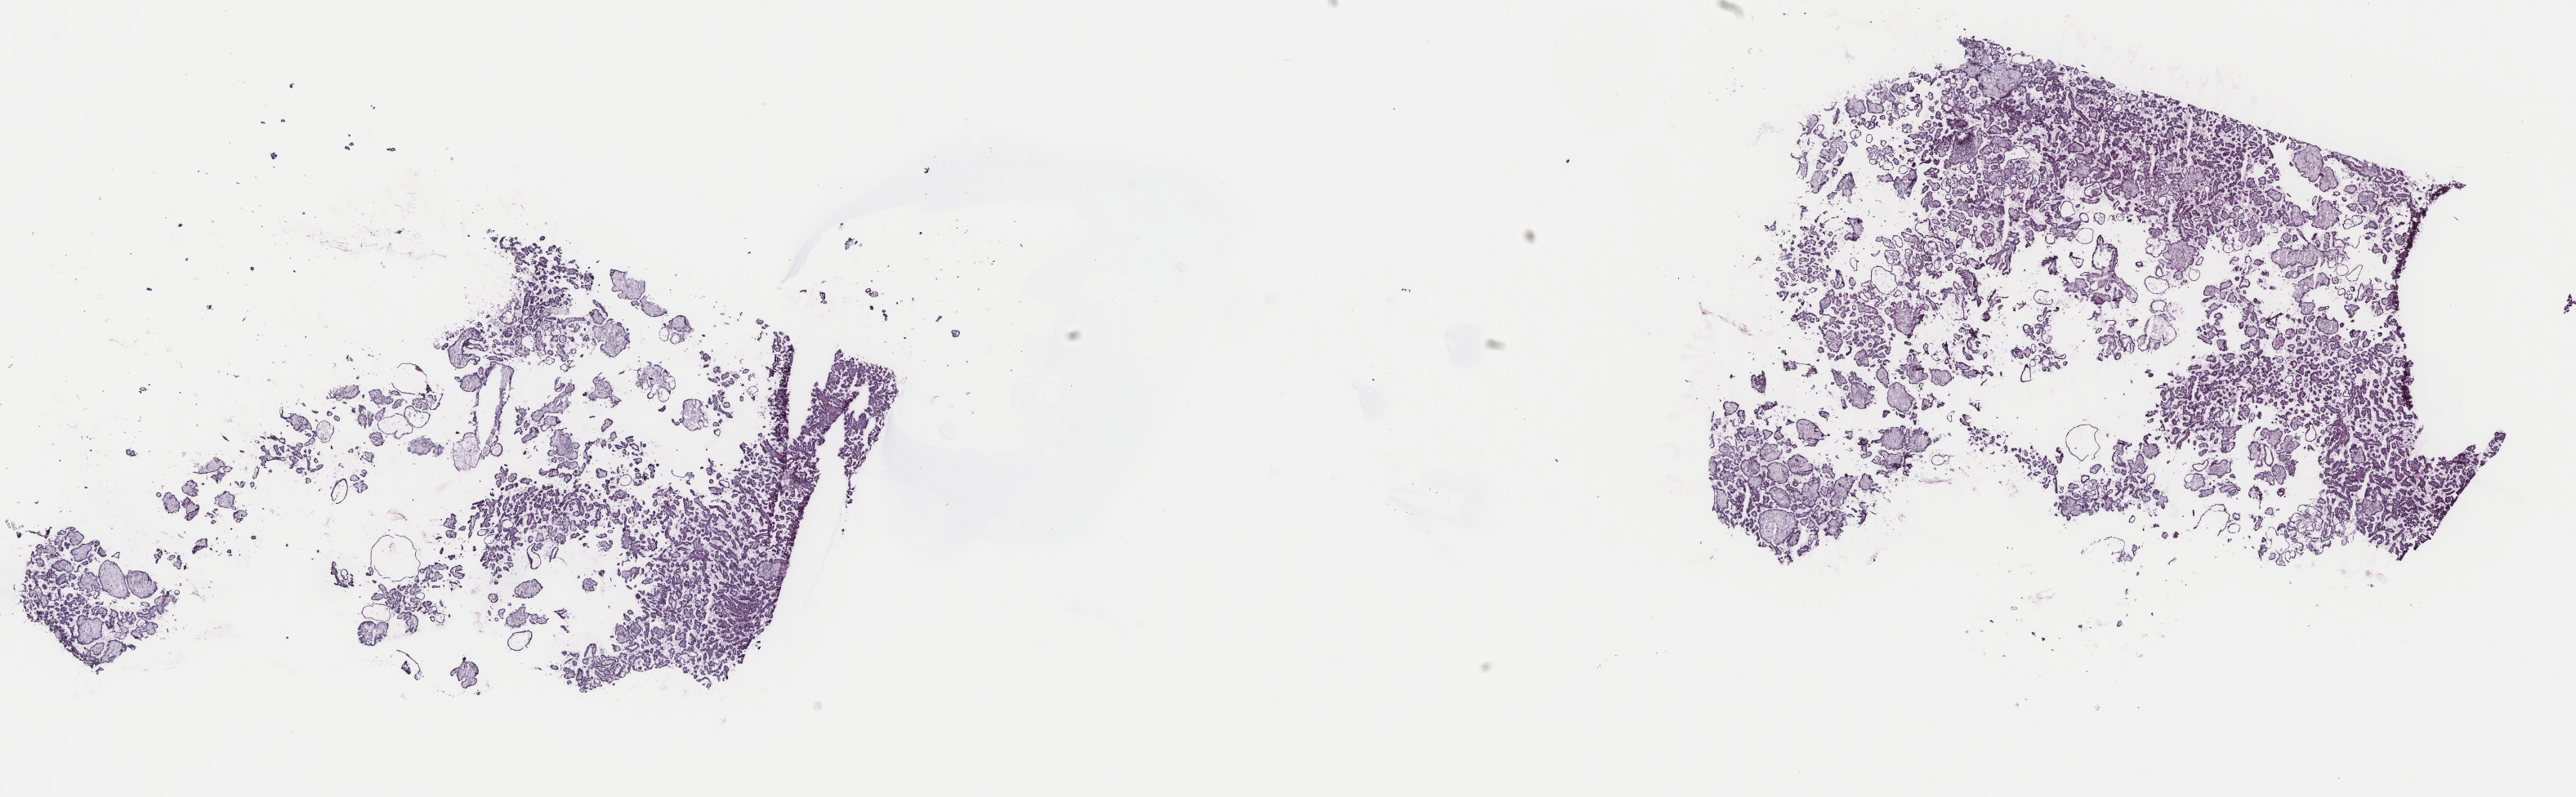
Digitized H&E tissue section (whole slide), low-resolution overview of the scanned area, about 25.0 x 7.7 mm (slide scanned at 40x), frozen section from the top of the tissue portion, kidney, primary tumour sample. Patient: male, age at initial diagnosis 65 years. Composition of this section per pathologist review: tumour cells 80%, tumour nuclei 80%, normal cells 0%, stromal cells 18%, necrosis 2%. Infiltration values recorded for this section: lymphocyte infiltration 3%, monocyte infiltration 8%, neutrophil infiltration 0%.
AJCC pathologic stage: I (7th edition). Pathologic diagnosis: Papillary adenocarcinoma, NOS.